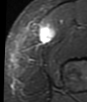
MRI of an extremity soft-tissue mass, one axial slice. Slice 12 of 48 in the series (ordered by position). STIR. MR volume resampled by the dataset authors to the PET/CT grid (not the native acquisition matrix). 3.27 mm slice thickness. 87 × 102 image matrix, field of view 85 × 100 mm. Female patient. From the clinical record (not read from this slice): histological type: synovial sarcoma; grade: intermediate; site of the primary tumour: right thigh.
Annotated regions visible in this slice (expert contour drawn on MRI and transferred to this co-registered scan by the dataset authors):
- gross tumour volume including surrounding oedema: bounding box <40,25,55,44> (left, top, right, bottom; pixels)
- gross tumour volume (mass): <38,25,55,44>